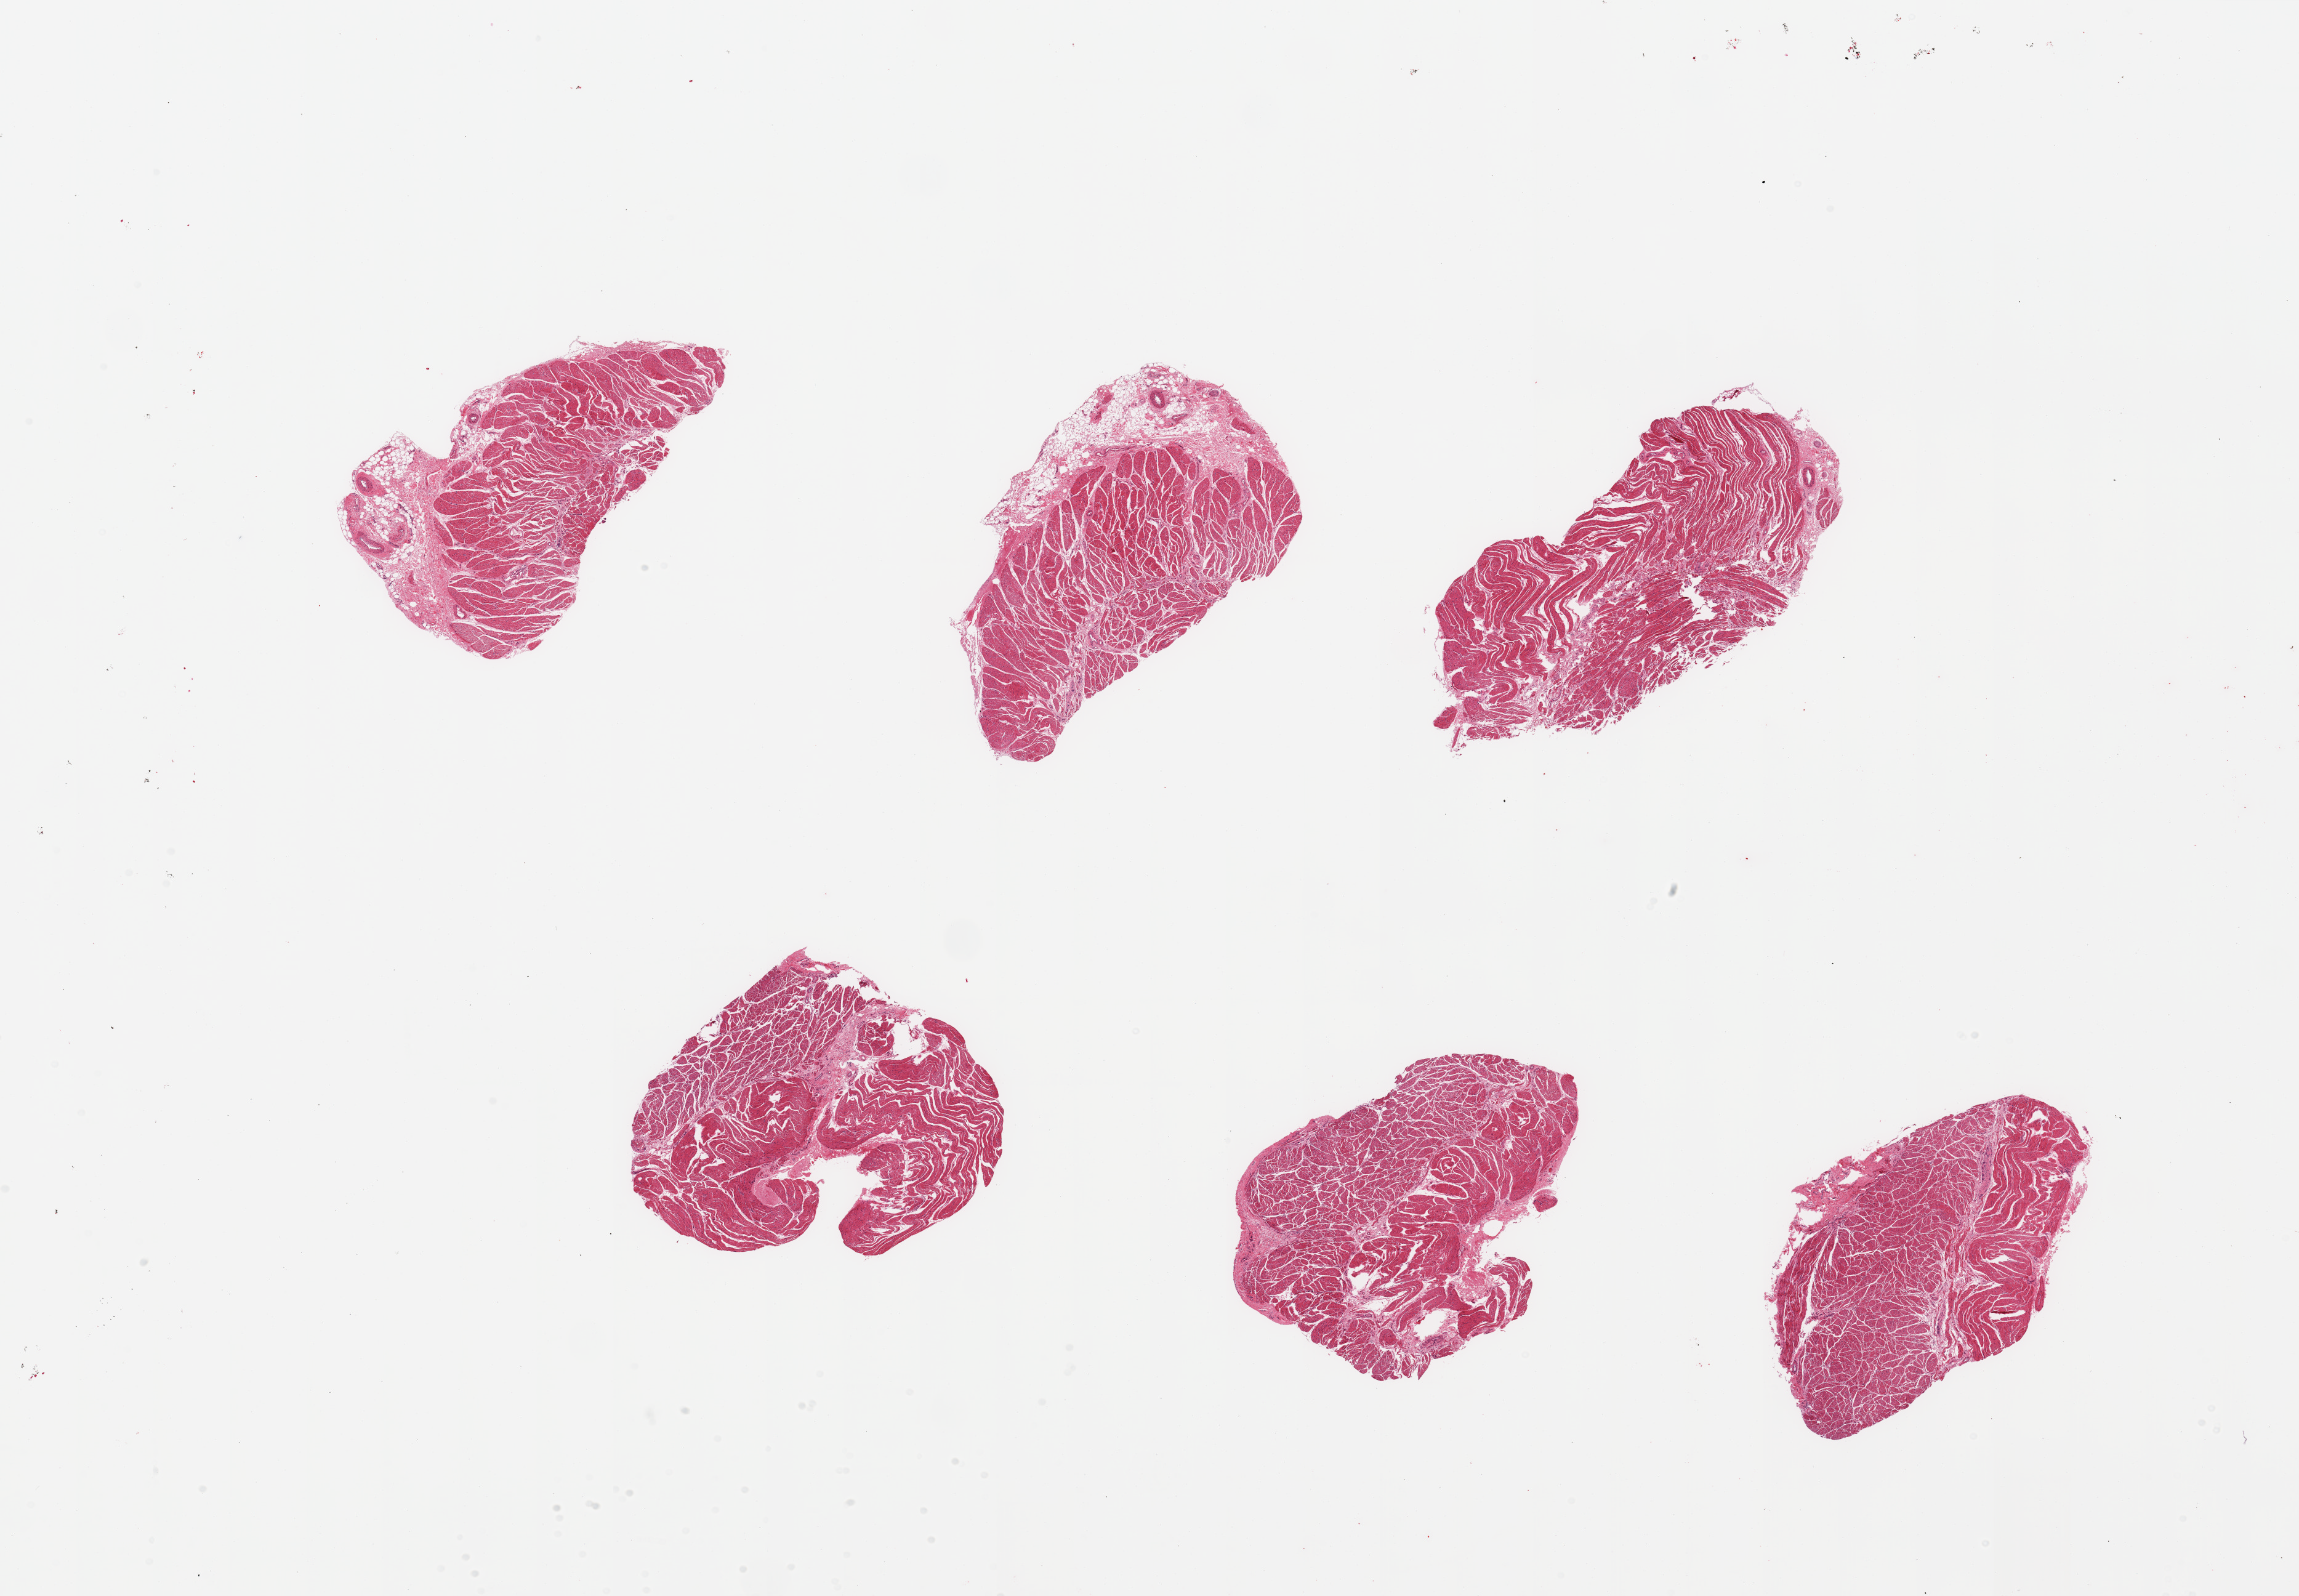
Digitized haematoxylin and eosin-stained section, brightfield — low-resolution overview of the scanned area, about 29.5 x 20.5 mm. PAXgene-fixed paraffin-embedded (PFPE) section. Target tissue: esophageal muscle. Tissue donor sample. Donor sex: male.
Review note (as recorded): 6 pieces, confirmed target muscularis, few peripheral nerve elements noted/.